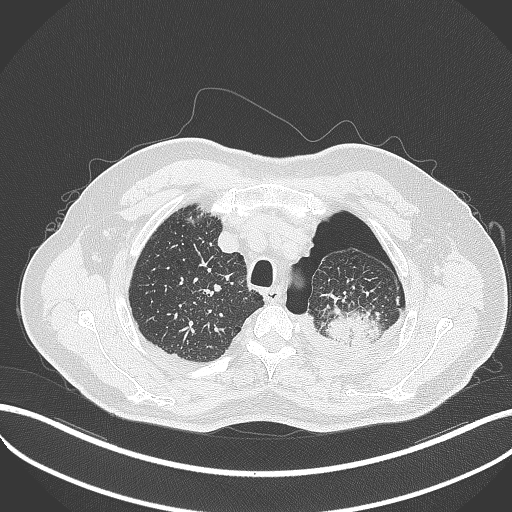
Chest CT, one axial slice. Slice 413 of 464 in the series (ordered by position). Lung window (W 1500 / L -600 HU). 1 mm slice thickness. 512 × 512 image matrix, field of view 400 × 400 mm. Patient: male, 76 years. Case-level facts recorded for this patient, not image findings: clinical TNM (as recorded): T3 N0 M1b.
Outlined on this slice (rectangle marked by the reading radiologist):
- lung tumour (recorded histology: adenocarcinoma): bounding box <326,300,382,348> (left, top, right, bottom; pixels)